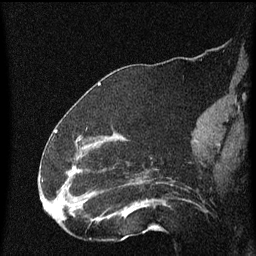
Breast MRI (dynamic contrast-enhanced), one sagittal slice; slice 29 of 60 in the series (ordered by position); dynamic contrast-enhanced series, image 2 of 4 at this slice position (ordered by acquisition); 1.5 T; TE 4.2 ms, TR 8 ms; 2 mm slice thickness; 256 × 256 image matrix. Female patient, age 52 years.
Outlined on this slice (semi-automatic segmentation, software-assisted and operator-edited):
- analysis volume of interest (the breast-tissue region the enhancement analysis was run in; not a lesion): box from (x=73, y=148) to (x=172, y=219) px
- tumour enhancement mask (voxels above the 70 % enhancement threshold inside the analysis volume of interest): (x=74, y=154)–(x=150, y=219)